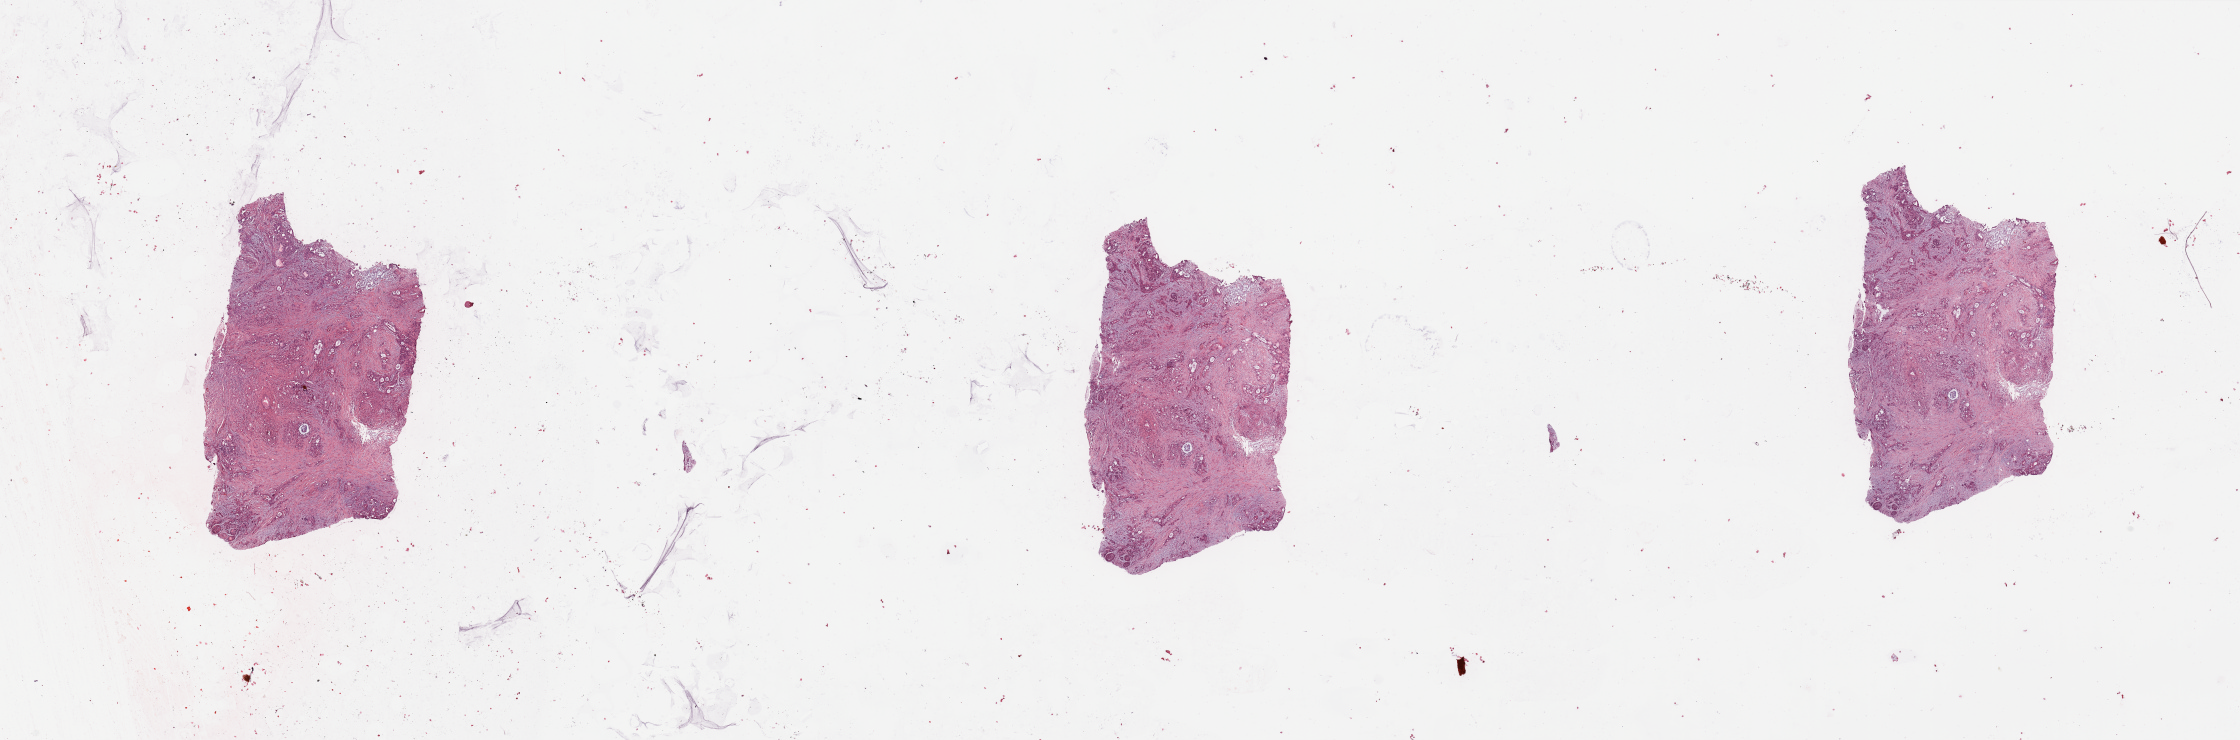
Digitized H&E tissue section (whole slide) — whole scanned area (about 35.4 x 11.7 mm, slide scanned at 20x) shown as a low-resolution overview; tumour tissue sample, sampled site: pancreas. Female, 43 y/o. Histologic grade: G2 (moderately differentiated). Slide review estimates, as recorded: tumour nuclei 30%, necrosis 0%.
AJCC pathologic stage: III. Primary tumour site (as recorded): head. Histologic diagnosis: Infiltrating duct carcinoma, NOS.